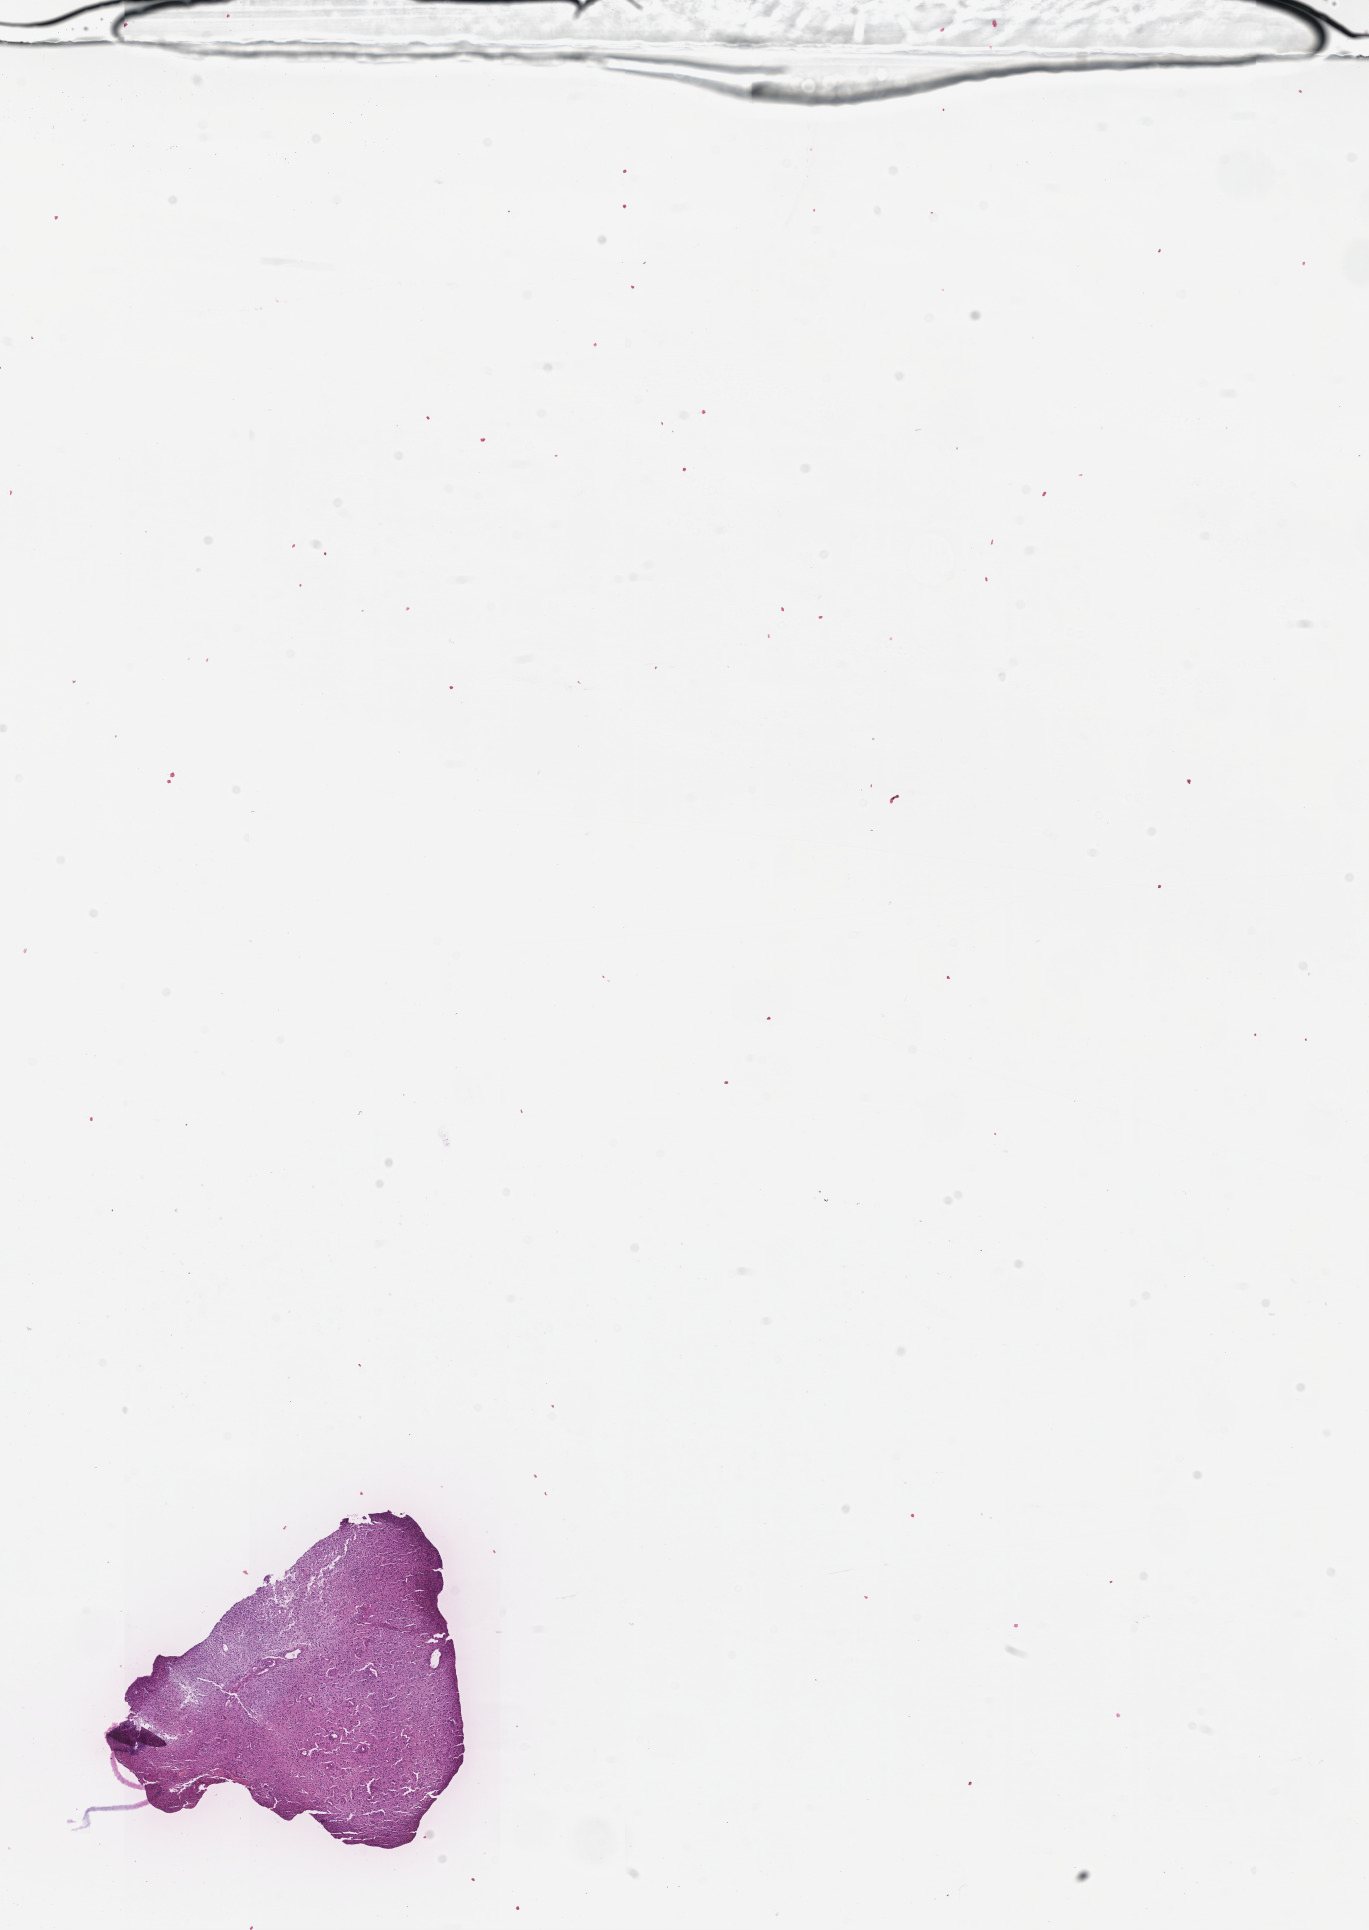
Digitized H&E tissue section (whole slide), low-resolution overview of the scanned area, about 11.0 x 15.6 mm (from a 20x scan); tumour tissue sample, sampled site: frontal lobe. Female, 75 y/o. Slide review estimates, as recorded: tumour nuclei 80%, necrosis 10%.
- primary tumour site (as recorded): frontal lobe
- diagnosis: Glioblastoma